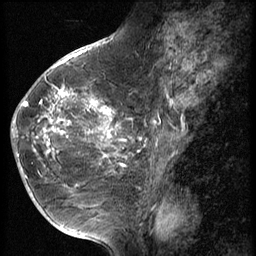
Breast MRI (dynamic contrast-enhanced), one sagittal slice. Position 27 of 56 along the scan axis. 3 images stored at this slice position (order not interpretable as contrast timing). 1.5 T. TE 4.2 ms, TR 9 ms. 2.5 mm slice thickness. 256 × 256 image matrix. Female patient, age 49 years. Case-level facts recorded for this patient, not image findings: setting: breast cancer imaged before/during neoadjuvant chemotherapy; receptor status: HER2-positive.
Annotated regions visible in this slice (semi-automatically segmented with operator editing):
- analysis volume of interest (the breast-tissue region the enhancement analysis was run in; not a lesion): box from (x=13, y=79) to (x=130, y=203) px
- tumour enhancement mask (voxels above the 140 % enhancement threshold inside the analysis volume of interest): (x=13, y=88)–(x=127, y=172)